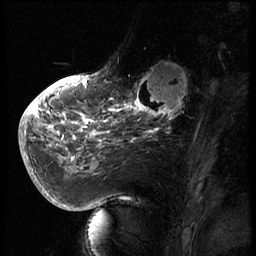
Breast MRI (dynamic contrast-enhanced), one sagittal slice. Position 22 of 66 along the scan axis. 3 images stored at this slice position (order not interpretable as contrast timing). 1.5 T. TE 4.2 ms, TR 8.9 ms. 2.5 mm slice thickness. 256 × 256 image matrix. Female patient, age 56 years. From the clinical record (not read from this slice): setting: breast cancer imaged before/during neoadjuvant chemotherapy.
Structures marked on this image (semi-automatically segmented with operator editing):
- analysis volume of interest (the breast-tissue region the enhancement analysis was run in; not a lesion): bounding box <129,62,194,127> (left, top, right, bottom; pixels)
- tumour enhancement mask (voxels above the 140 % enhancement threshold inside the analysis volume of interest): <129,65,189,127>